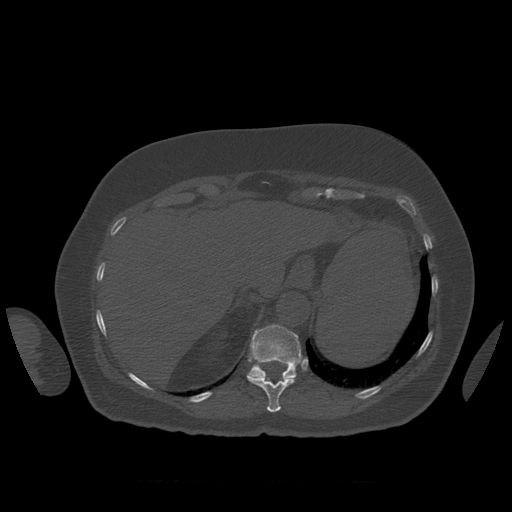
CT including the spine, one axial slice; reconstruction kernel STANDARD; bone window (W 1800 / L 400 HU); 512 × 512 image matrix, field of view 404 × 404 mm. Patient age 81 years. From the clinical record (not read from this slice): primary cancer: renal; vertebrae with lytic lesions (as recorded): L1.
Structures marked on this image (semi-automatic segmentation, software-assisted and operator-edited):
- T11 vertebra: bounding box (x1, y1, x2, y2) in pixels: (247, 376, 296, 413)
- T12 vertebra: (247, 325, 303, 381)